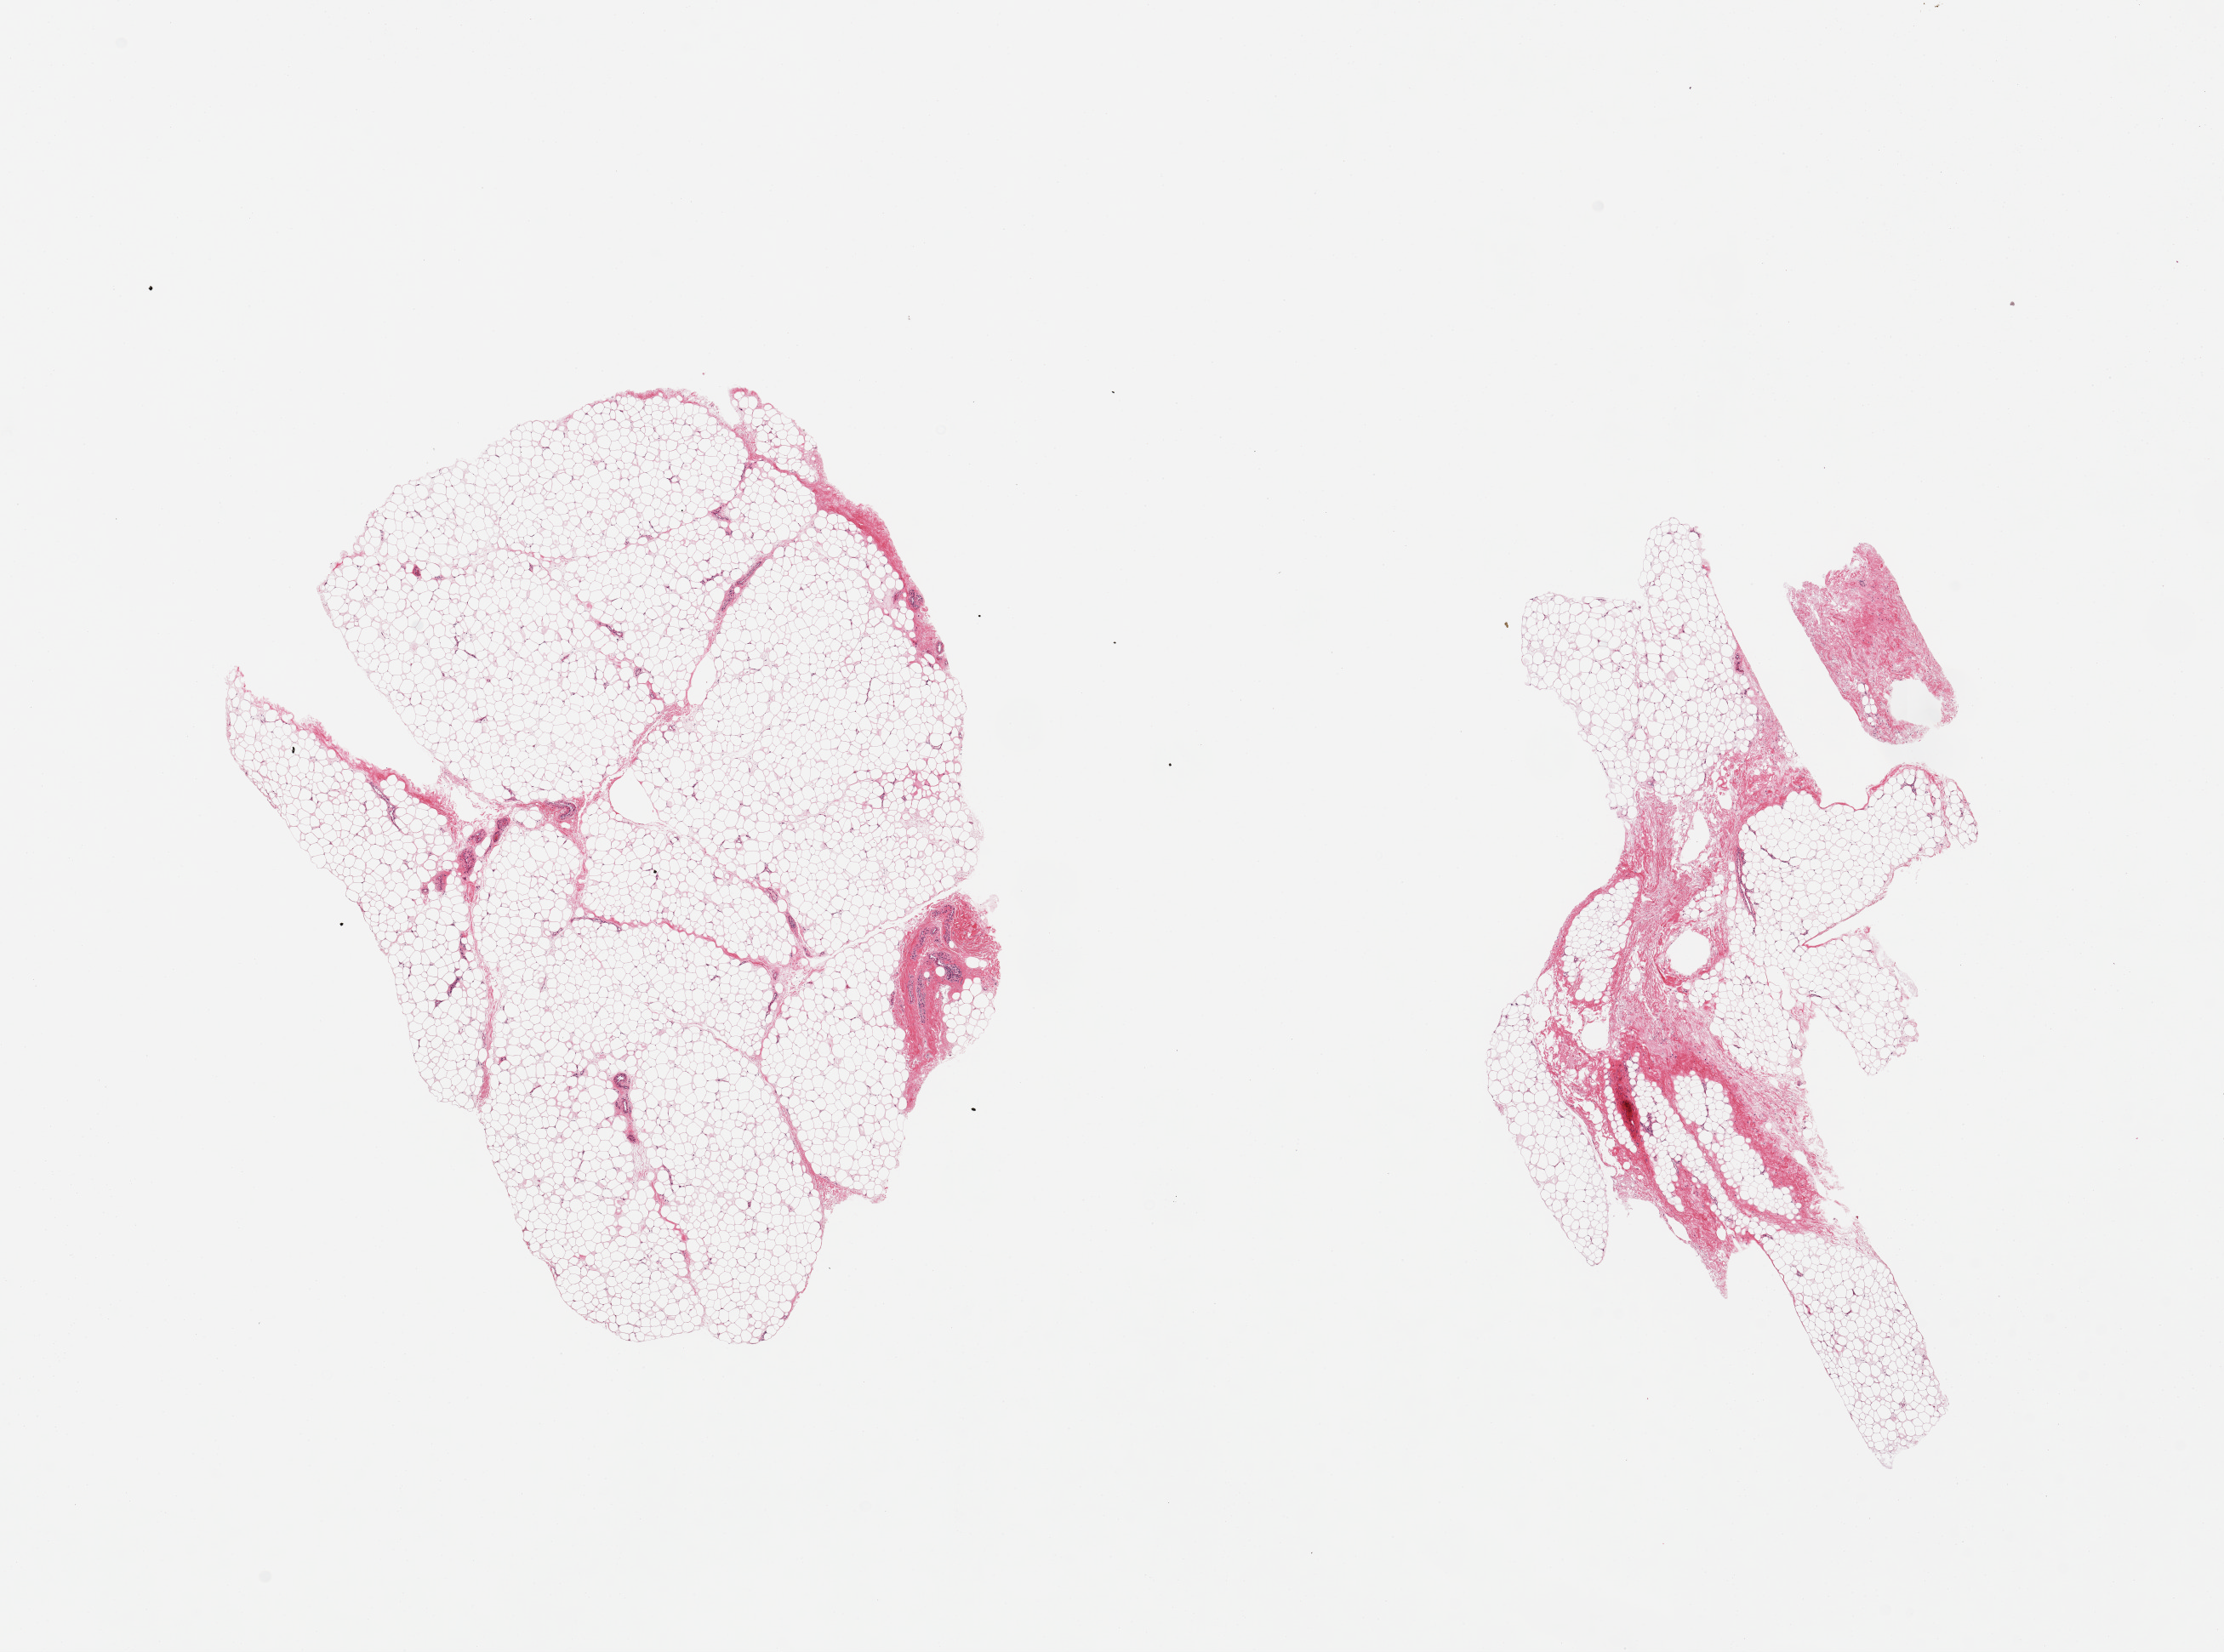
Whole-slide image, hematoxylin and eosin (H&E) stain, brightfield, low-resolution overview of the scanned area, about 20.7 x 15.4 mm, PAXgene-fixed paraffin-embedded (PFPE) section, sampled site (target tissue): adipose tissue, donor tissue sample. Donor: male.
Reviewer comment on this tissue sample: 2 pieces; 5 and 20% fibrous stroma.